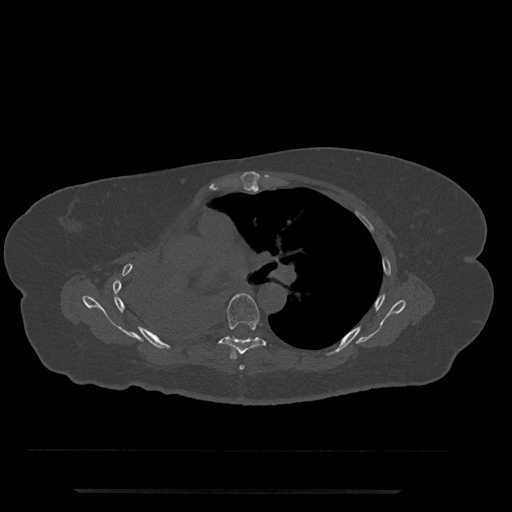
CT including the spine, one axial slice; position 496 of 797 along the scan axis; reconstruction kernel Br40s/3; 120 kVp; bone window (W 1800 / L 400 HU); 512 × 512 image matrix. Female patient, age 51 years. Case-level facts recorded for this patient, not image findings: primary cancer: neuro.
Structures marked on this image (semi-automatic segmentation, software-assisted and operator-edited):
- T5 vertebra: box from (x=239, y=365) to (x=245, y=370) px
- T6 vertebra: (x=218, y=293)–(x=273, y=360)